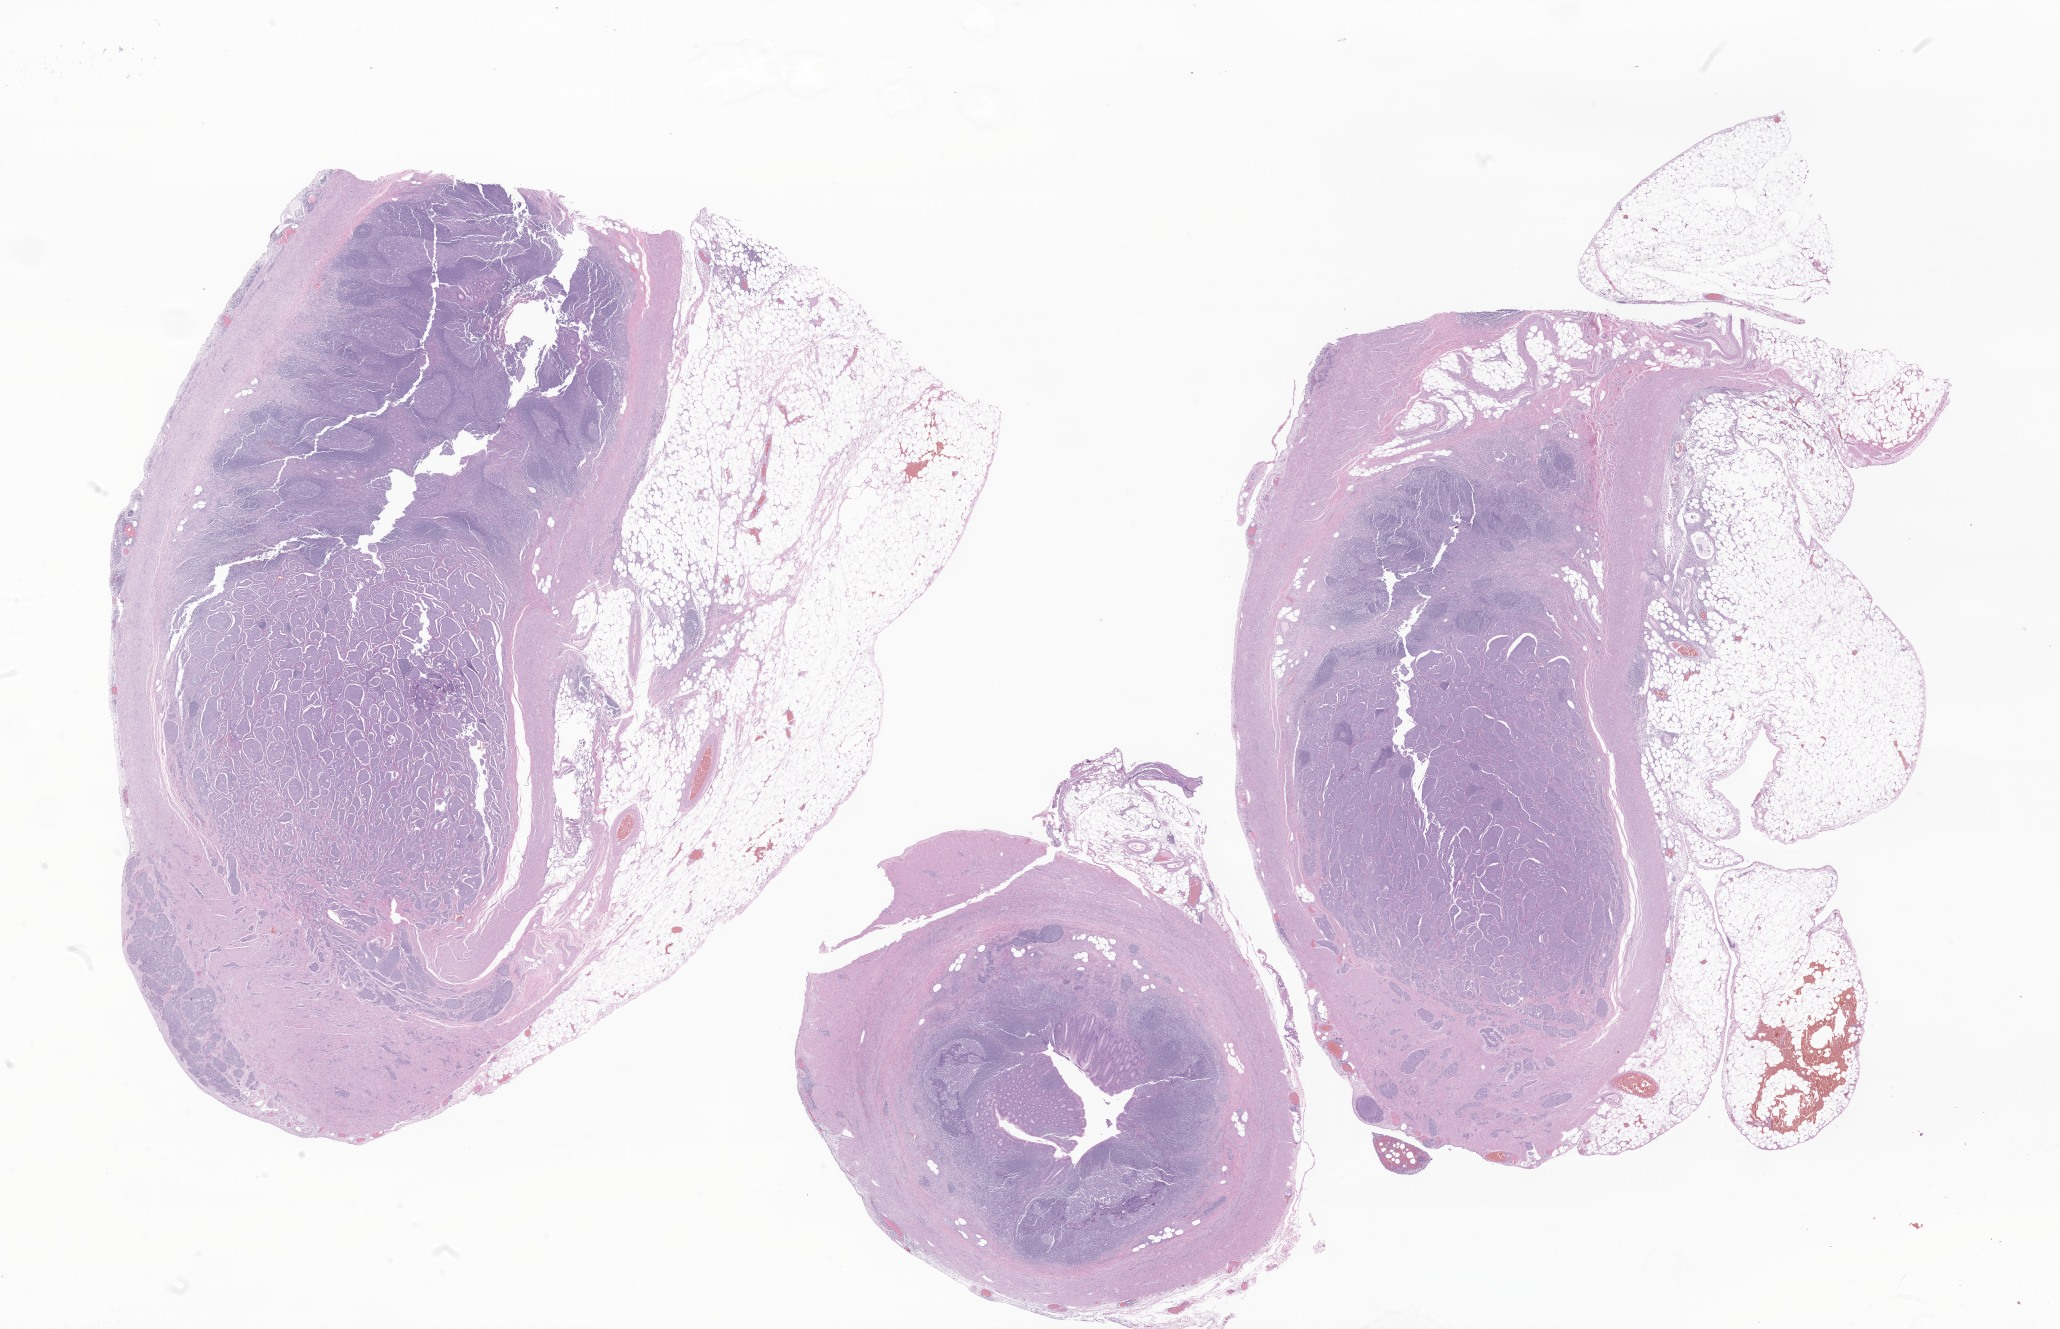
Hematoxylin and eosin (H&E) whole-slide image of tumor tissue from the appendix, whole scanned area (about 34.7 x 22.4 mm) shown as a low-resolution overview. FFPE section. Patient male; age 205 months (17 years 1 month).
• diagnosis: Neuroendocrine carcinoma, NOS